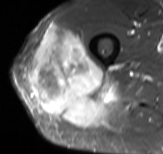
MRI of an extremity soft-tissue mass, one axial slice; position 45 of 61 along the scan axis; STIR; MR volume resampled by the dataset authors to the PET/CT grid (not the native acquisition matrix); 3.27 mm slice thickness; 163 × 154 image matrix, field of view 159 × 150 mm. Male patient. Case-level facts recorded for this patient, not image findings: histological type: poorly differentiated synovial sarcoma; grade: high; site of the primary tumour: right buttock.
Annotated regions visible in this slice (expert contour drawn on MRI and transferred to this co-registered scan by the dataset authors):
- gross tumour volume including surrounding oedema: bounding box <29,25,115,124> (left, top, right, bottom; pixels)
- gross tumour volume (mass): <29,25,111,124>